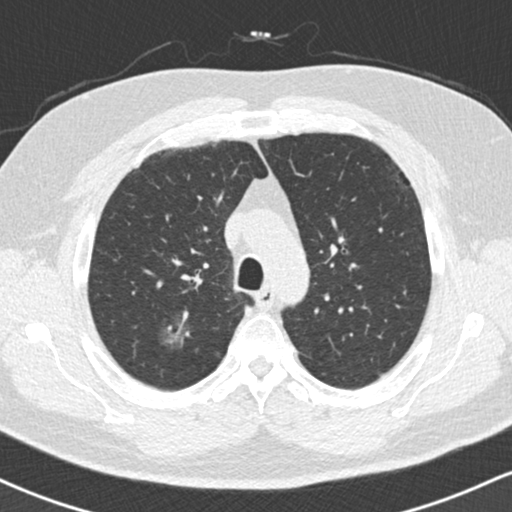
Low-dose screening chest CT, one axial slice. Position 124 of 169 along the scan axis. Reconstruction kernel B30f. Lung window (W 1500 / L -600 HU). 2 mm slice thickness. 512 × 512 image matrix, field of view 320 × 320 mm.
Outlined on this slice (manually delineated by an expert):
- lesion 1 (tumor, upper lobe of right lung): bounding box <161,323,190,346> (left, top, right, bottom; pixels)